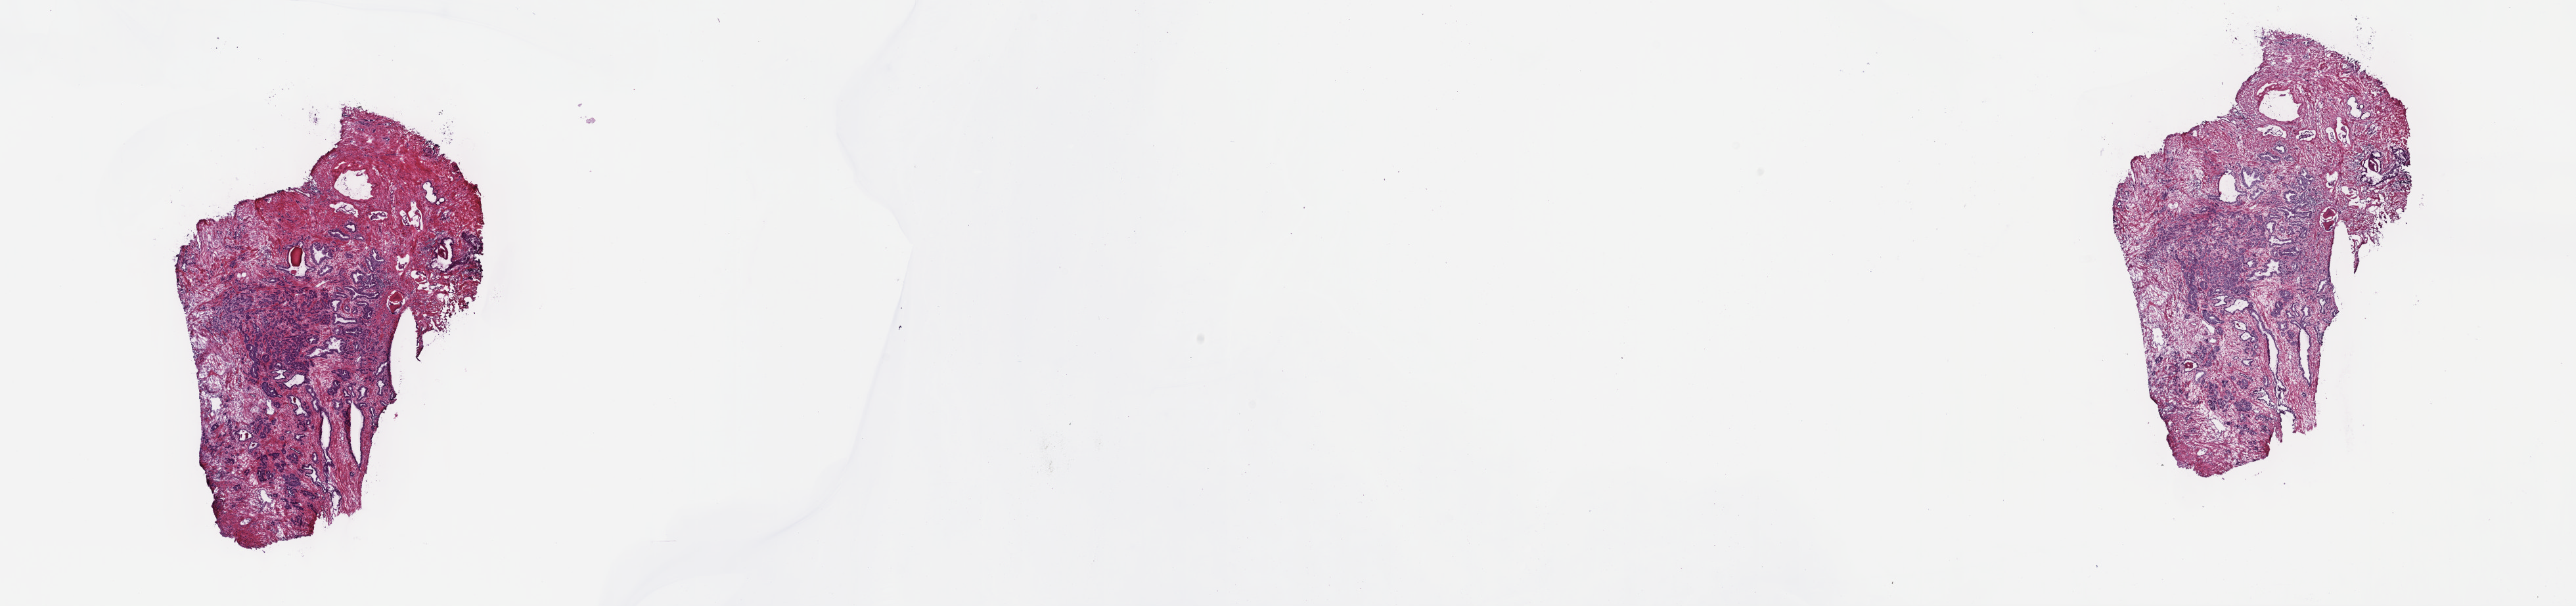
Digitized H&E tissue section (whole slide) — a low-resolution overview of the entire scanned area, about 31.7 x 7.5 mm (slide scanned at 40x), frozen section, sample: primary tumour, prostate. Male patient; age at initial diagnosis 61 years. Gleason score: 7 (3+4). Slide review estimates, as recorded: tumour cells 70%, tumour nuclei 70%, normal cells 0%, stromal cells 20%, necrosis 10%. Inflammatory infiltration, as recorded: lymphocyte infiltration 40%, monocyte infiltration 20%, neutrophil infiltration 20%.
Lymph nodes positive (case pathology): 0 of 10 examined. Histologic diagnosis: Adenocarcinoma, NOS (prostate gland).